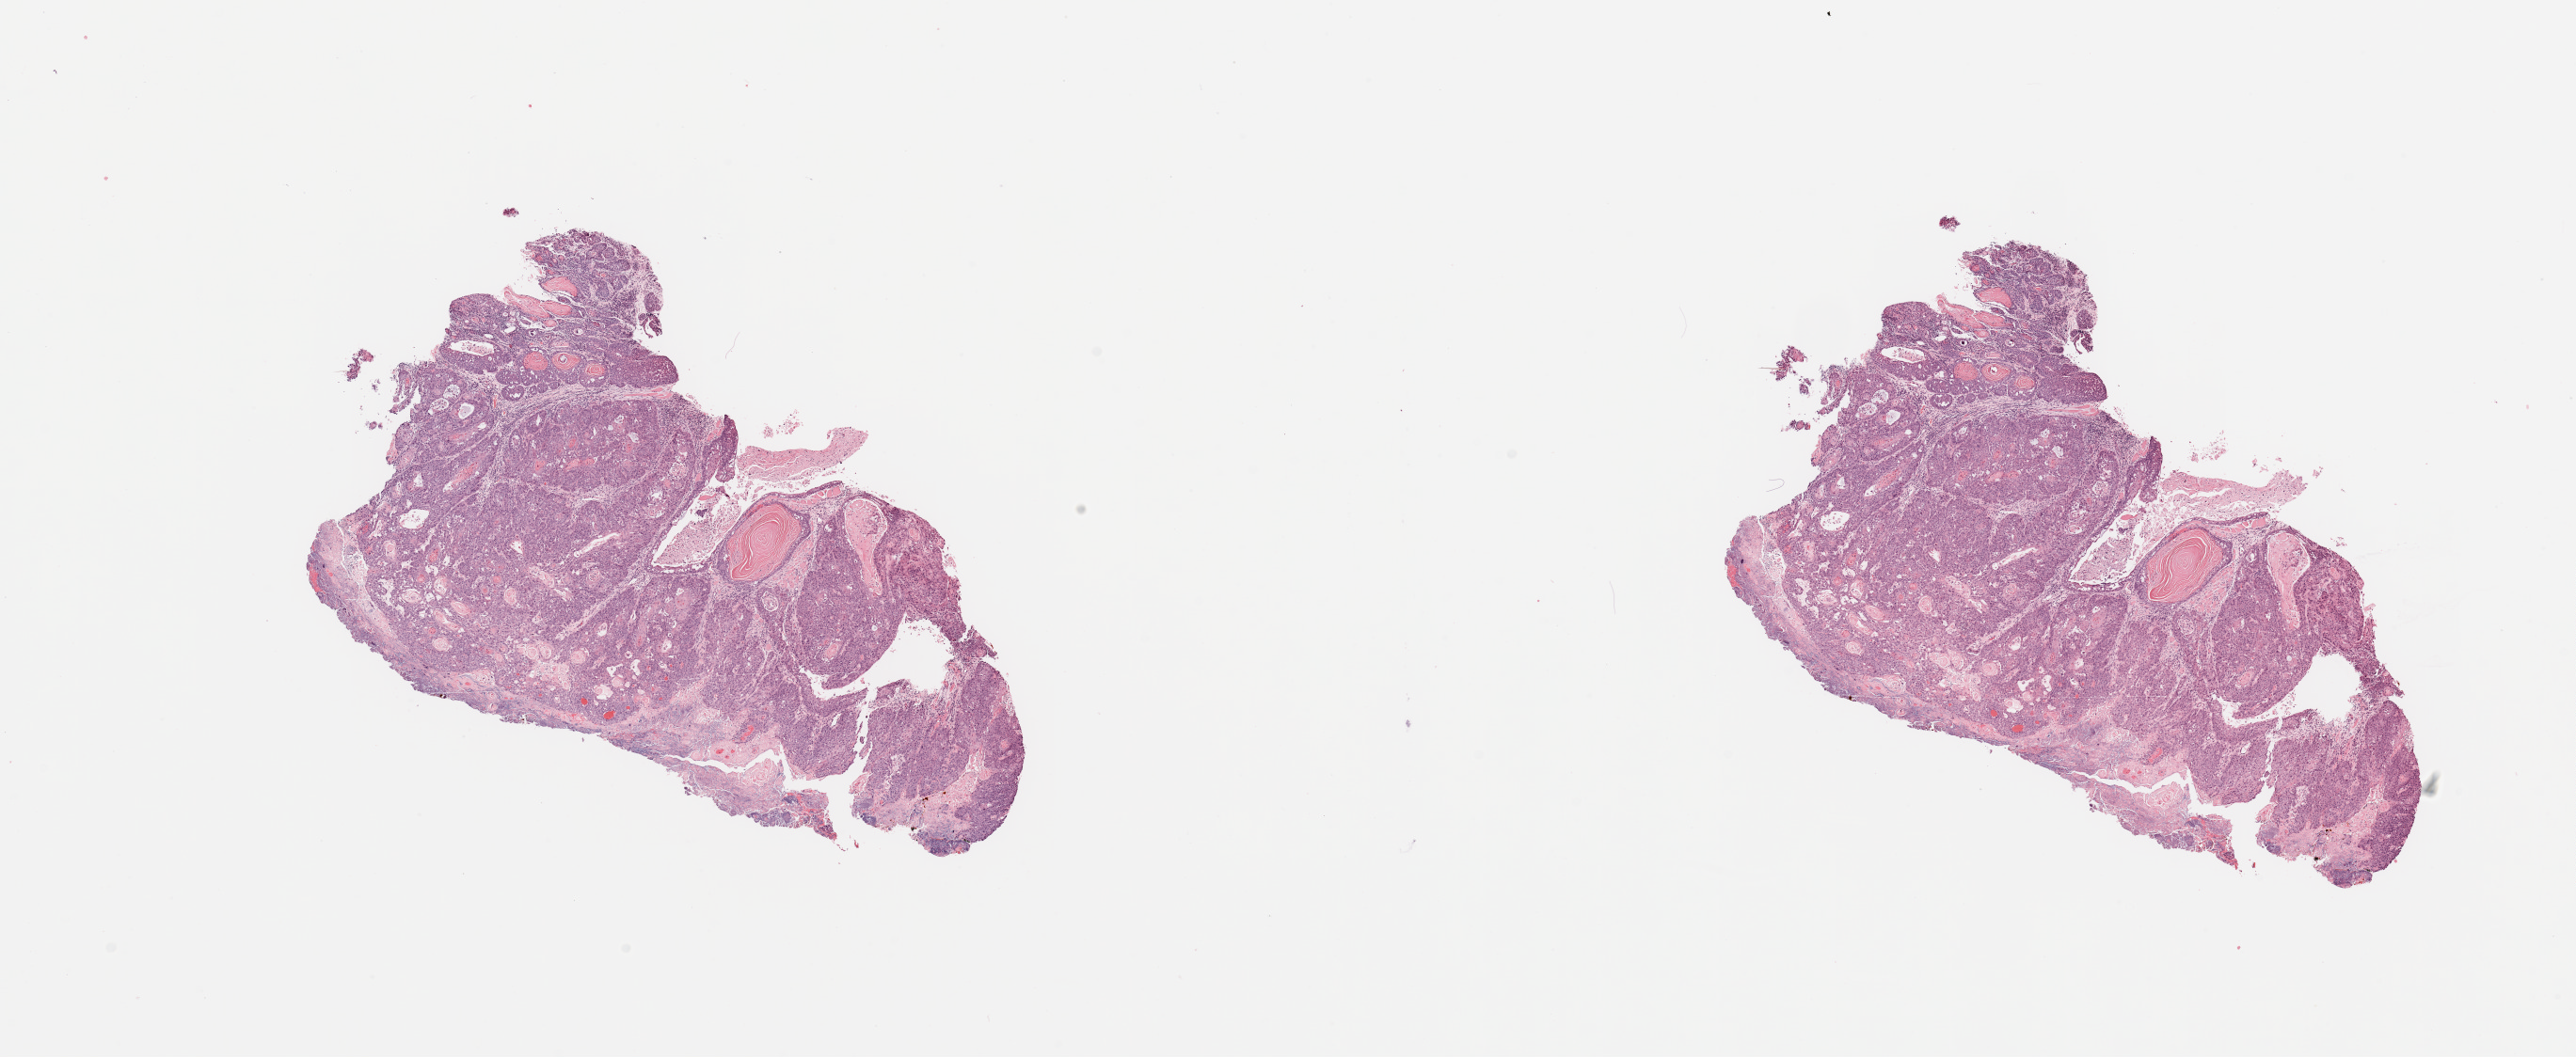
Whole-slide histology image, H&E-stained, a low-resolution overview of the entire scanned area, about 21.7 x 8.9 mm (slide scanned at 20x). Tumour tissue sample, sampled site: tongue. 77-year-old male patient. Histologic grade: G1 (well differentiated). Composition of this section per pathologist review: tumour nuclei 90%, necrosis 7%.
• primary tumour site (as recorded): oral cavity
• AJCC pathologic stage: III
• diagnosis: Squamous cell carcinoma, NOS (tongue, NOS)